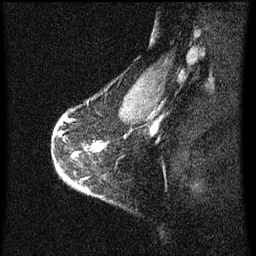
Breast MRI (dynamic contrast-enhanced), one sagittal slice; position 50 of 60 along the scan axis; dynamic contrast-enhanced series, image 2 of 3 at this slice position (ordered by acquisition); 1.5 T; TE 4.2 ms, TR 8 ms; 256 × 256 image matrix, field of view 180 × 180 mm. Patient: female, 56 years.
Annotated regions visible in this slice (semi-automatic segmentation, software-assisted and operator-edited):
- analysis volume of interest (the breast-tissue region the enhancement analysis was run in; not a lesion): bounding box [x1, y1, x2, y2] px = [56, 112, 105, 193]
- tumour enhancement mask (voxels above the 70 % enhancement threshold inside the analysis volume of interest): [96, 144, 103, 151]